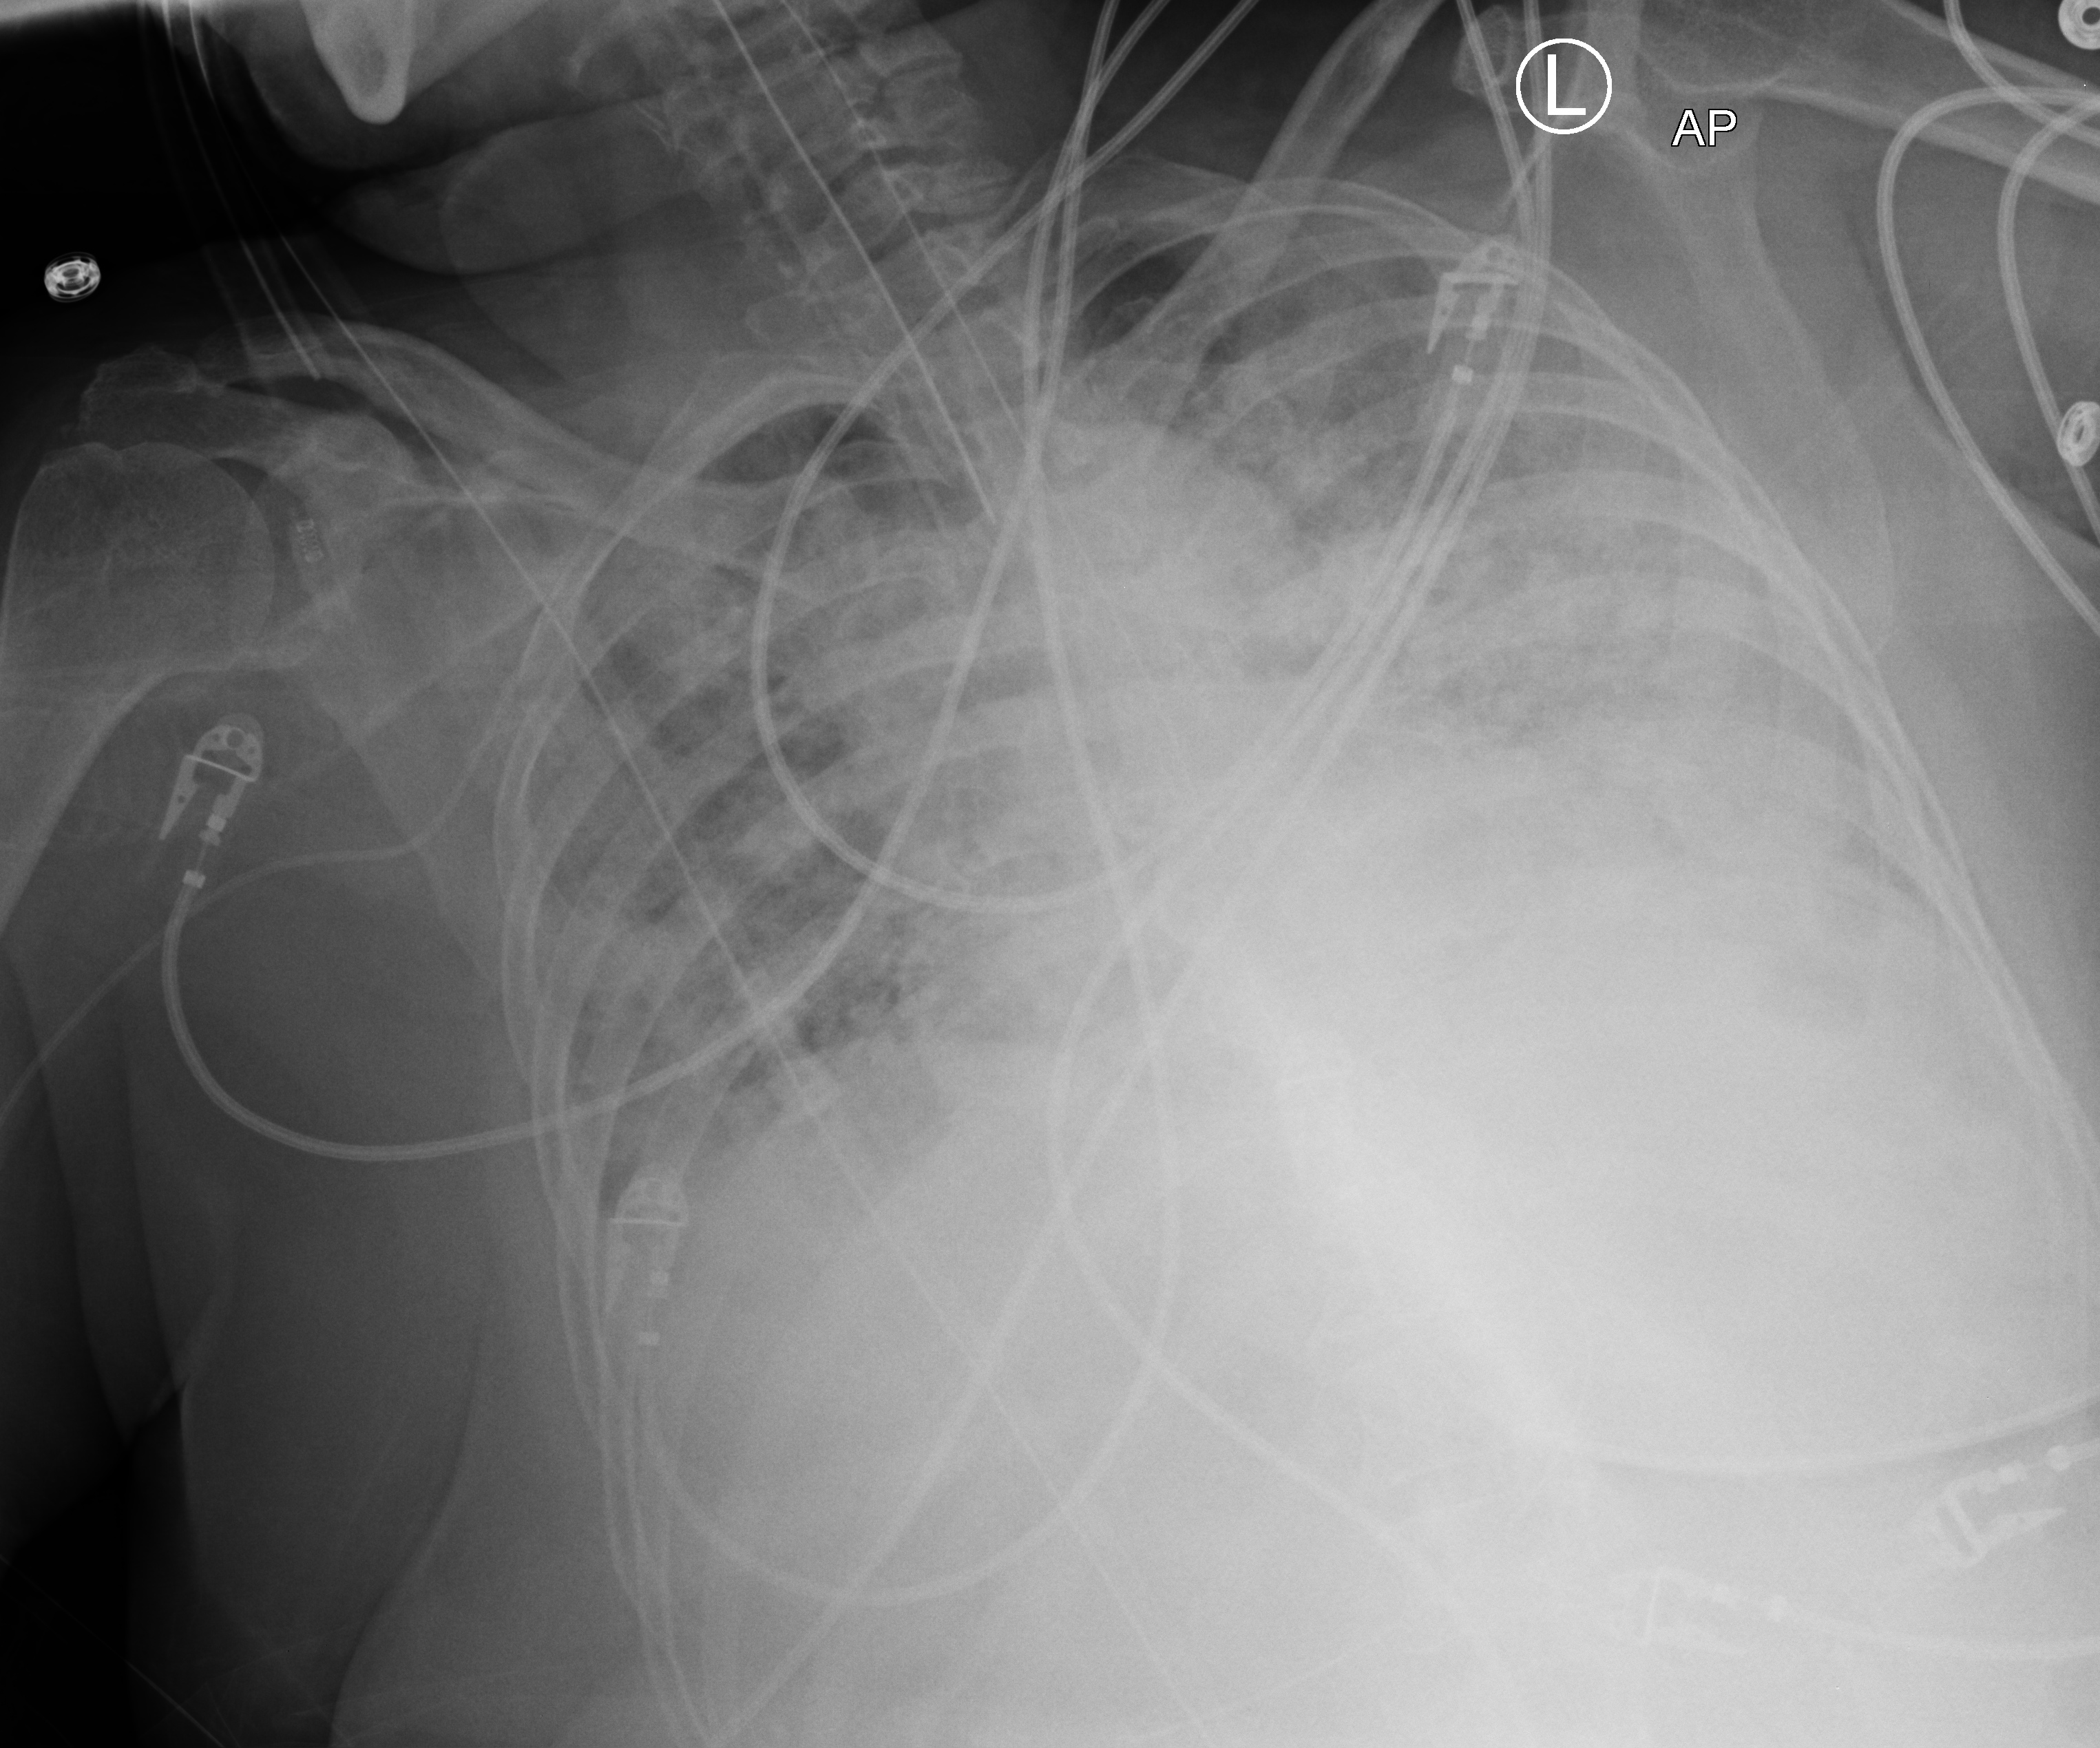
Chest X-ray (portable); anteroposterior (AP) projection. Patient hospitalised with COVID-19; female, aged 75–90 years.
From the hospital-stay record, not from the radiograph (when in the stay this image was taken is not recorded): admitted to intensive care during this hospital stay: yes; diabetes (admission record): yes; mechanically ventilated during this hospital stay: yes.